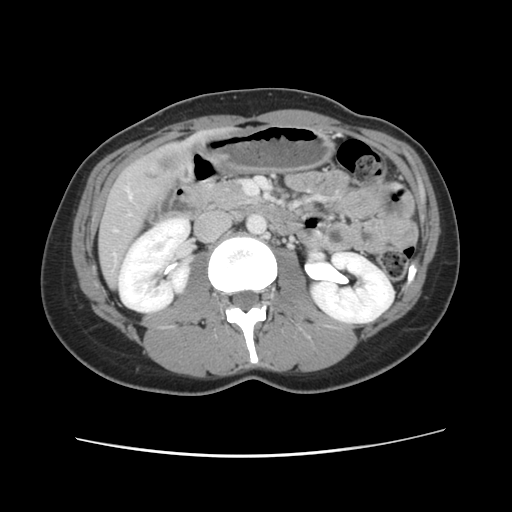
Contrast-enhanced abdominal CT, one axial slice; position 33 of 134 along the scan axis; 120 kVp; intravenous contrast given; soft-tissue window (W 400 / L 40 HU); 512 × 512 image matrix. Female patient, age 33 years. Case-level facts recorded for this patient, not image findings: diagnosis: colorectal cancer liver metastases, imaged before liver resection; multiple liver metastases: yes.
Outlined on this slice (outlined manually by an expert reader):
- hepatic veins: box from (x=128, y=191) to (x=132, y=198) px
- liver: (x=99, y=131)–(x=226, y=287)
- planned liver remnant (the part of the liver to remain after resection): (x=99, y=242)–(x=121, y=287)
- liver metastasis: (x=141, y=153)–(x=192, y=184)